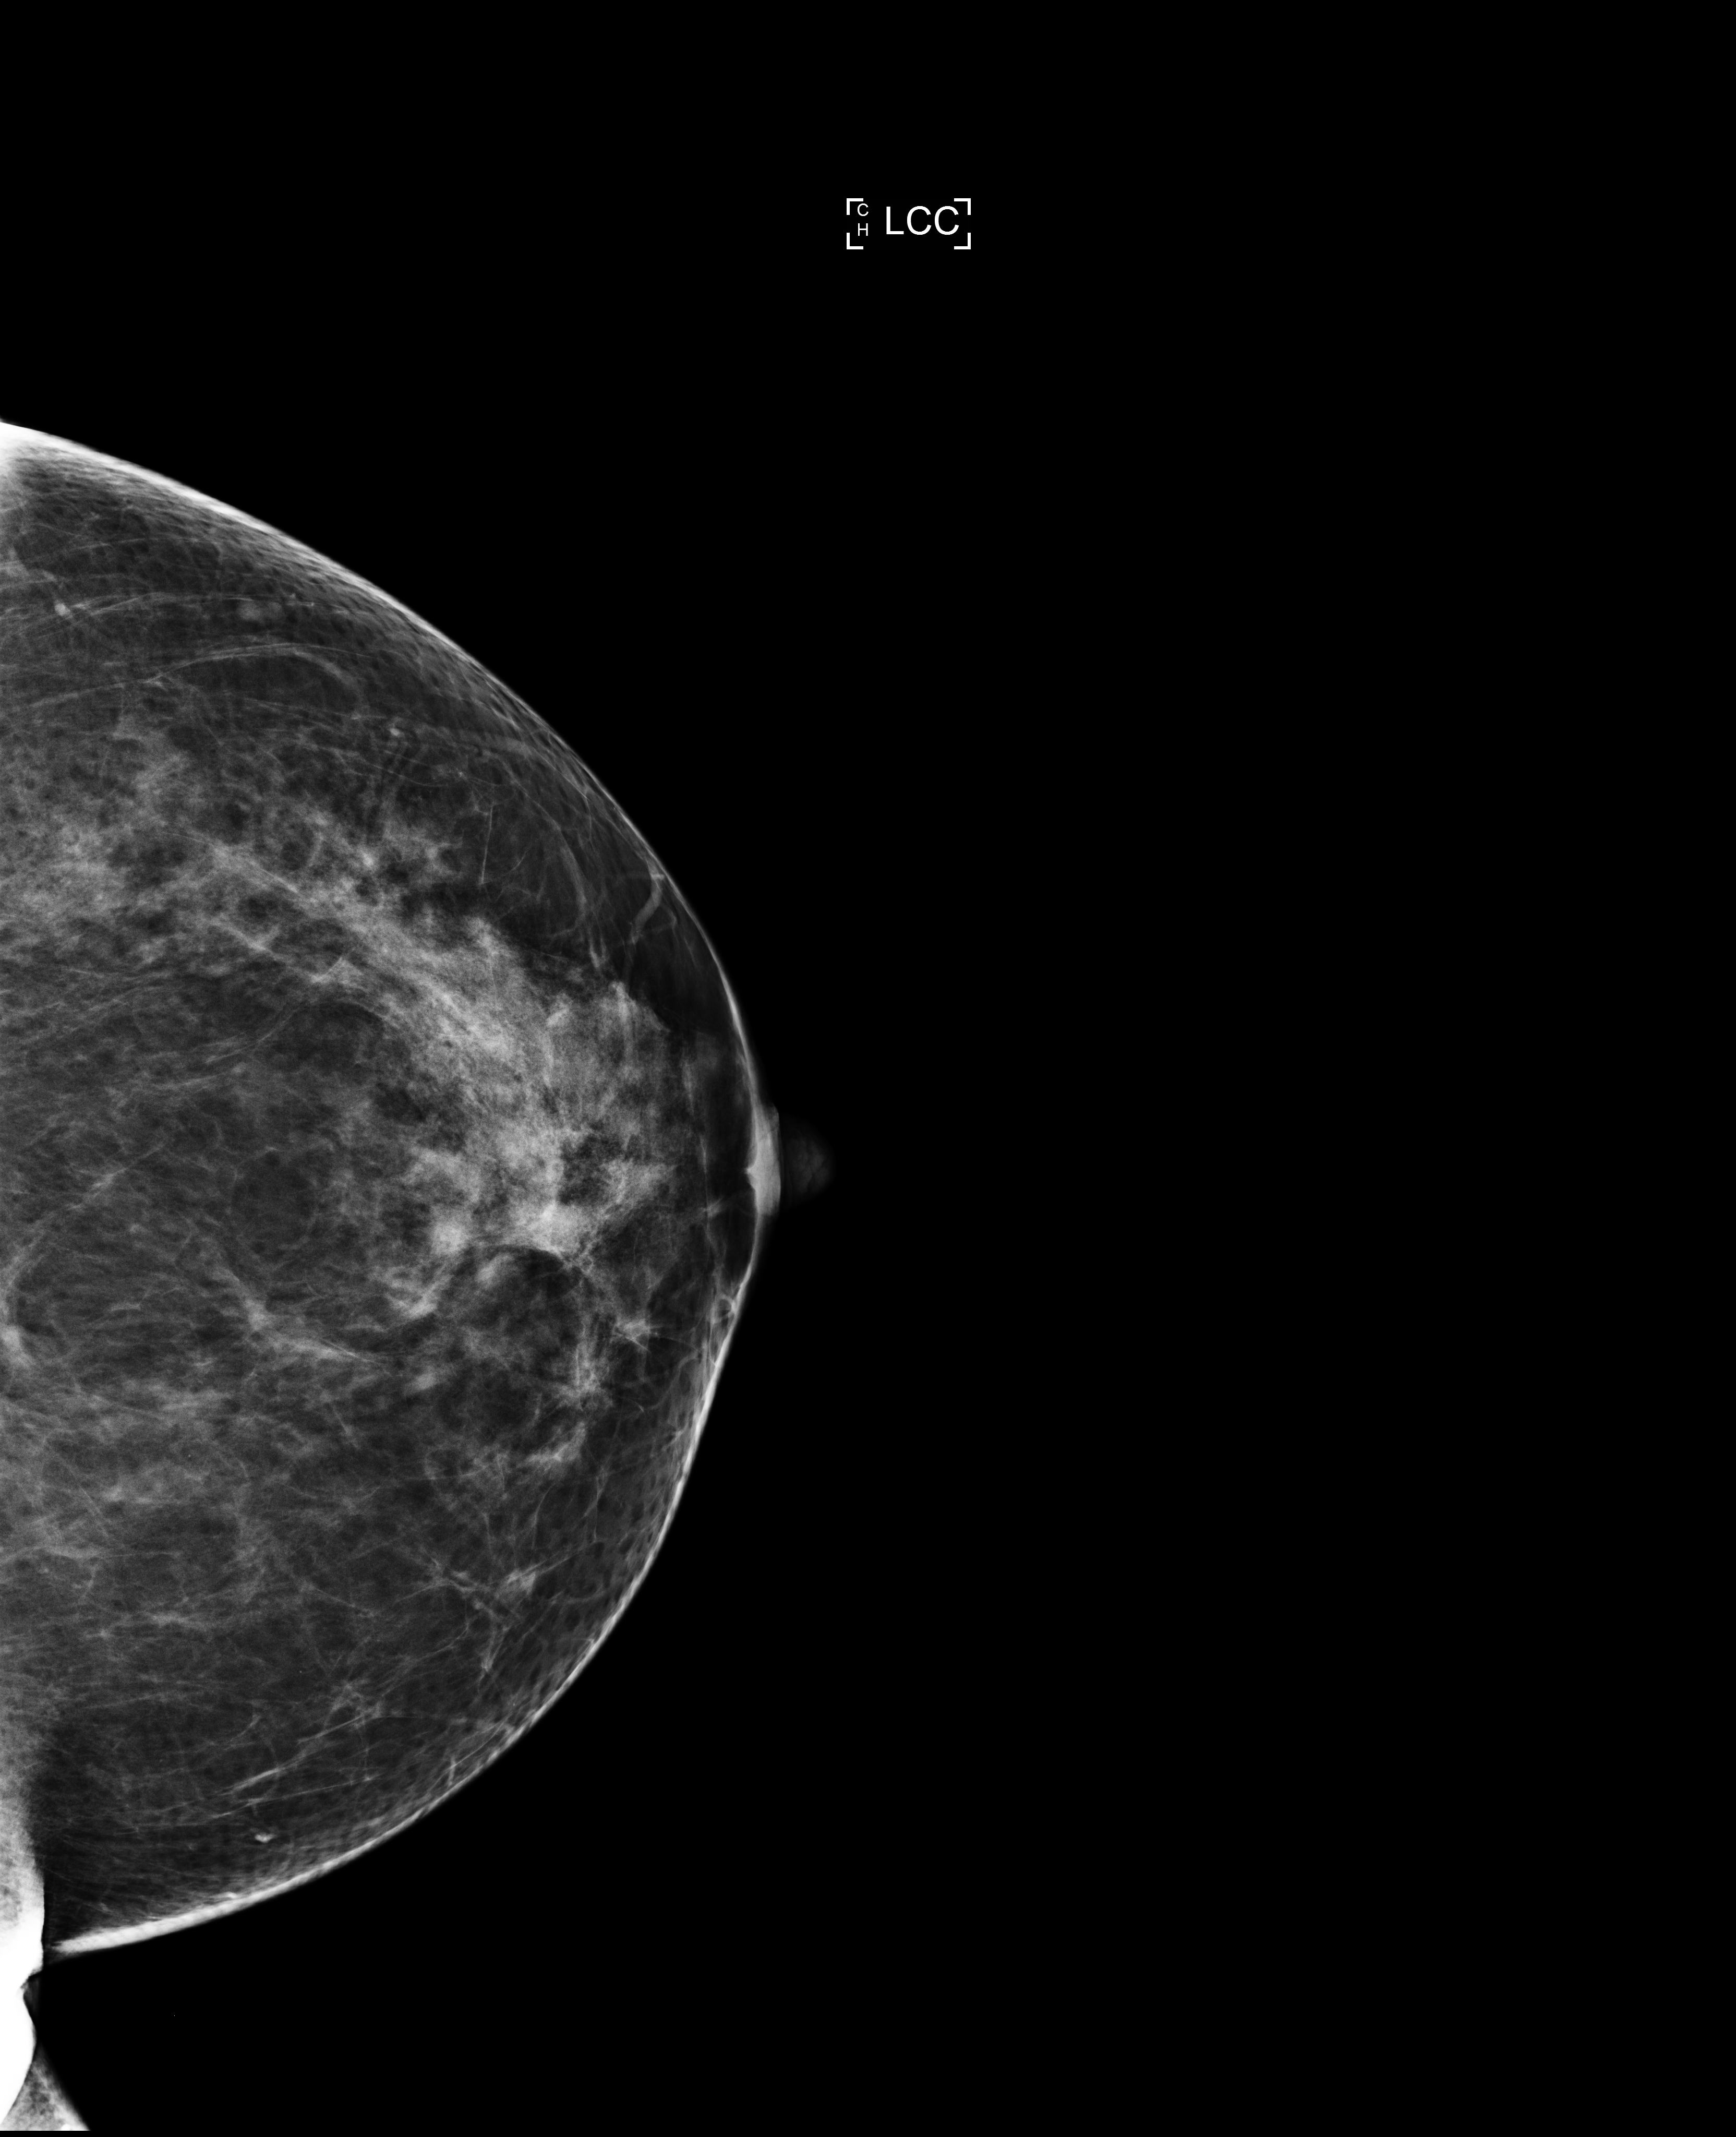
Full-field digital mammogram (FFDM), left breast, craniocaudal (CC) view, screening examination, compressed breast thickness 83 mm. Patient aged 49 years (female).
Breast density at the screening exam (both breasts): heterogeneously dense (BI-RADS density category c).